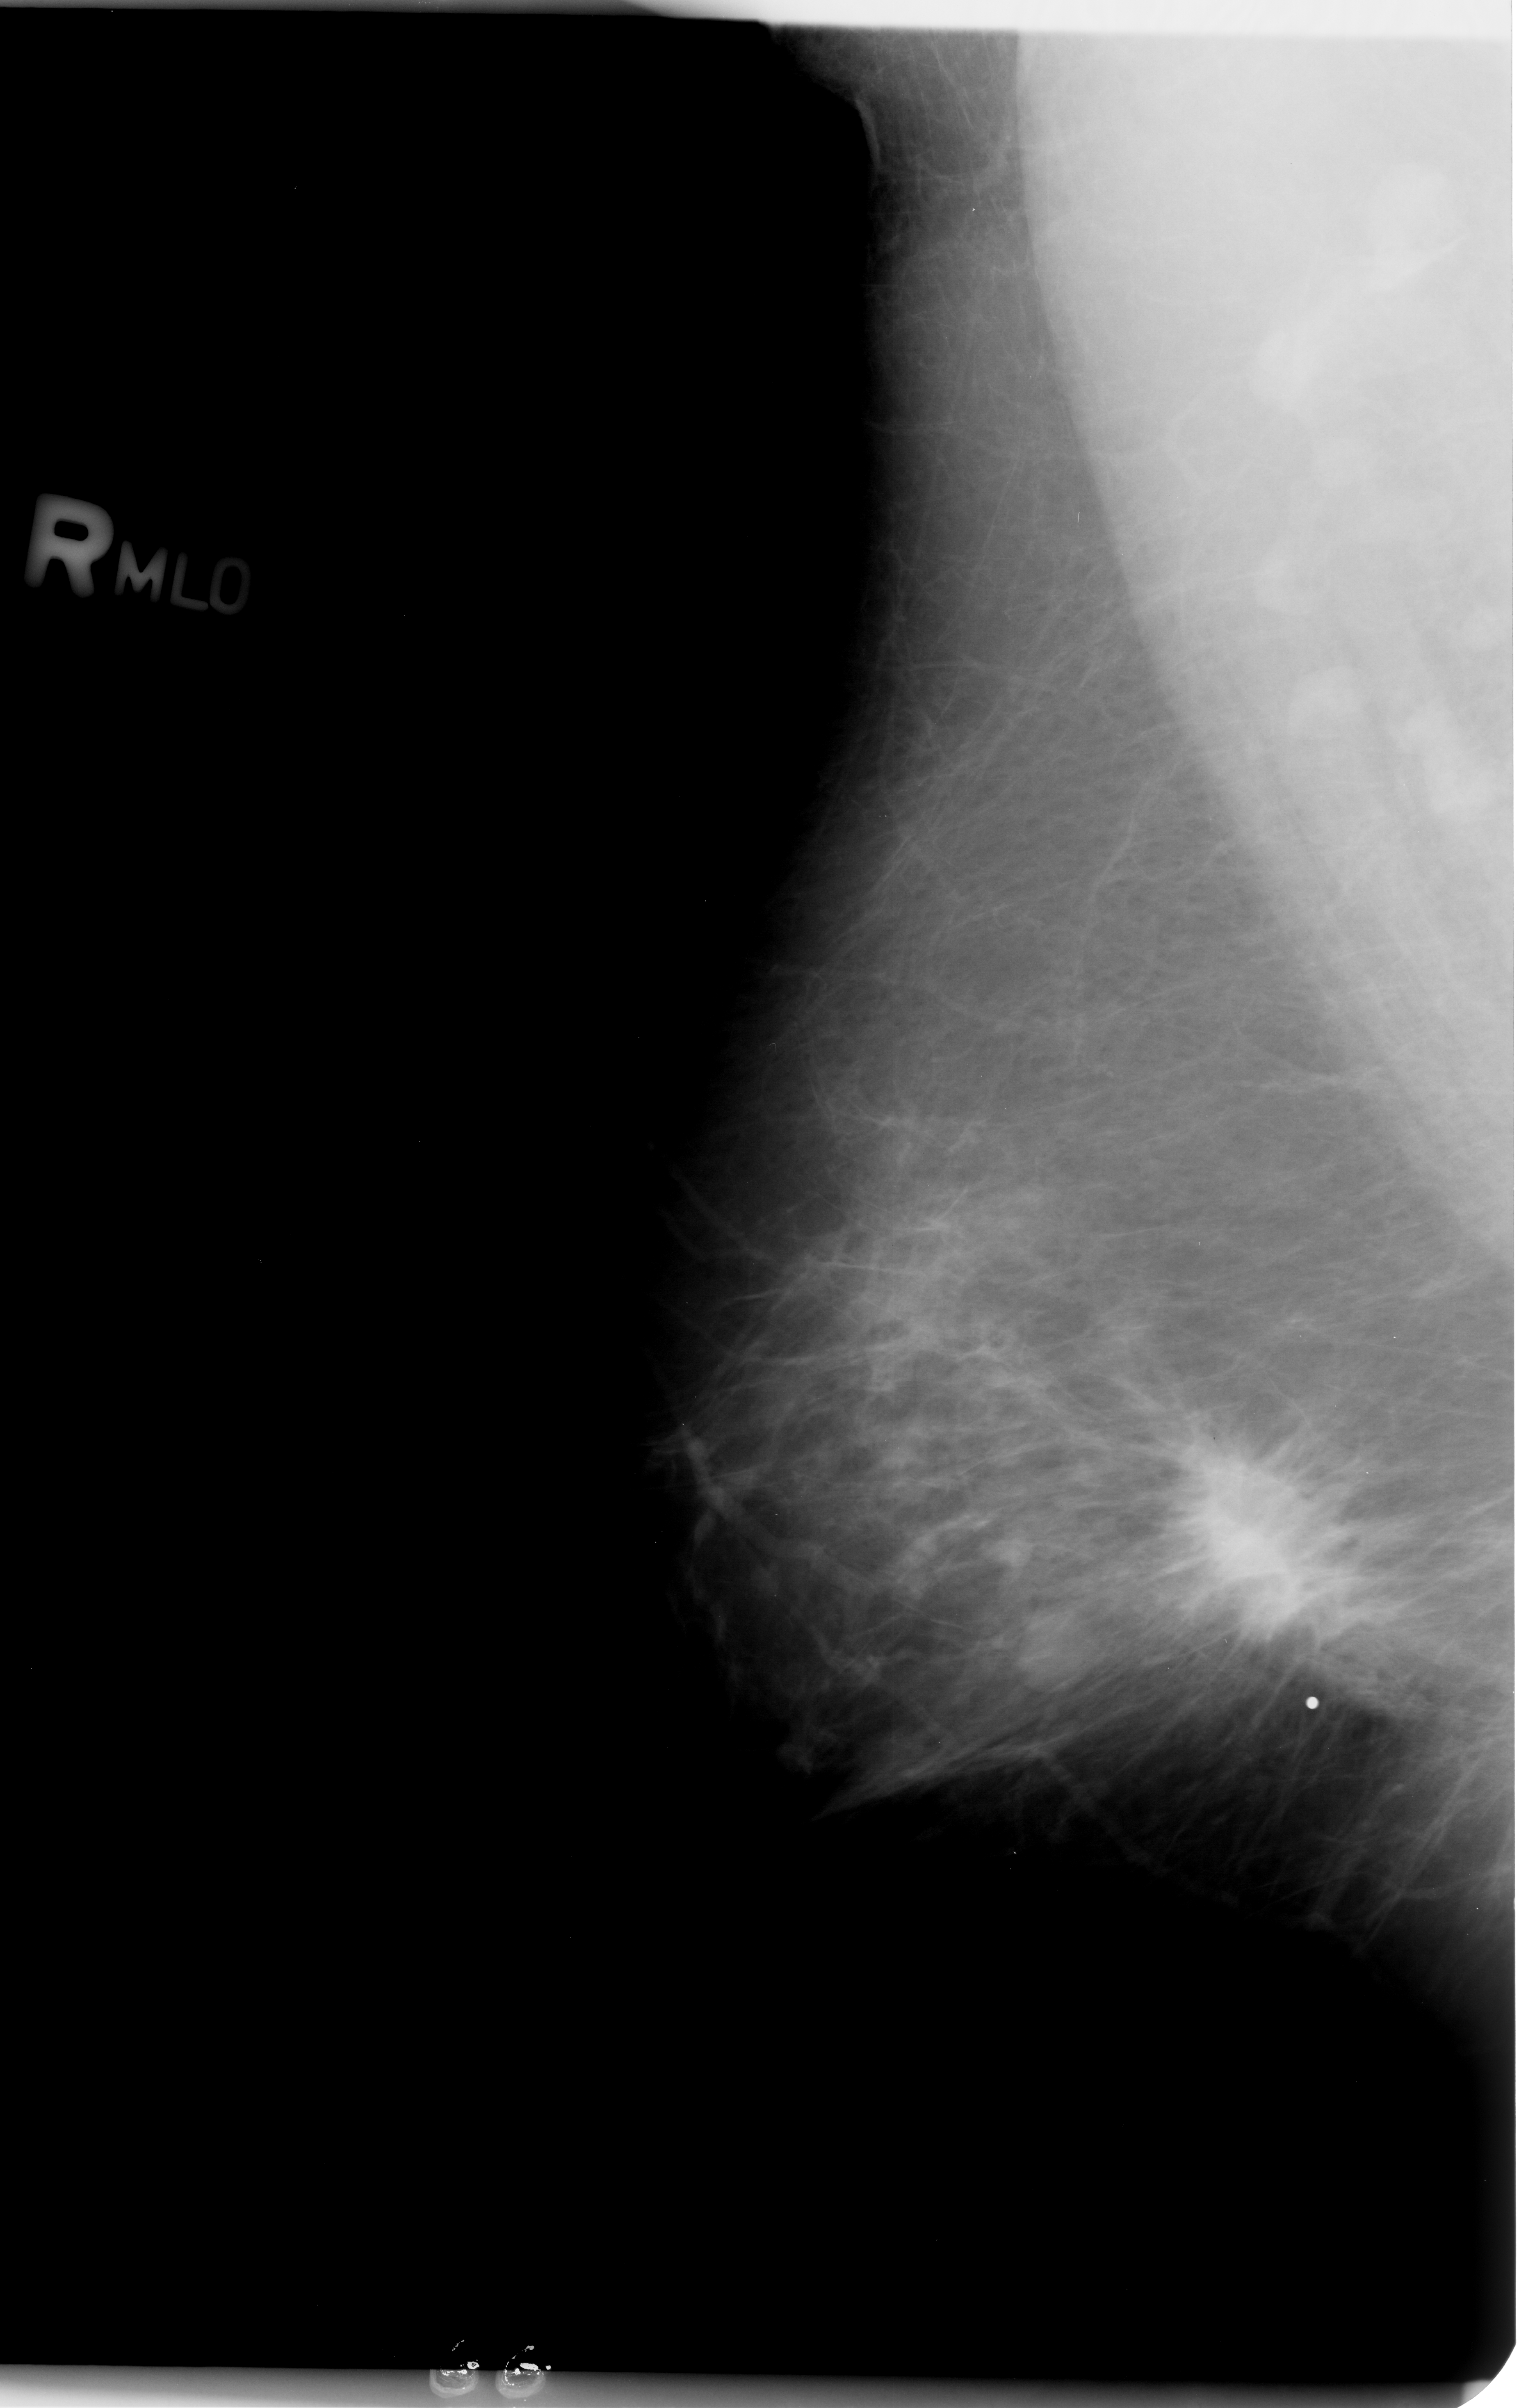
Digitized screen-film mammogram; right breast; MLO view; BI-RADS breast density category 2 (scale 1–4); 1519 × 2408 image matrix.
Expert-marked regions of interest on this image (one box per marked abnormality):
- mass, shape irregular / architectural distortion, margins spiculated; BI-RADS assessment category 5; pathology result (as recorded, not read from the image): malignant: bounding box (x1, y1, x2, y2) in pixels: (1153, 1470, 1371, 1651)